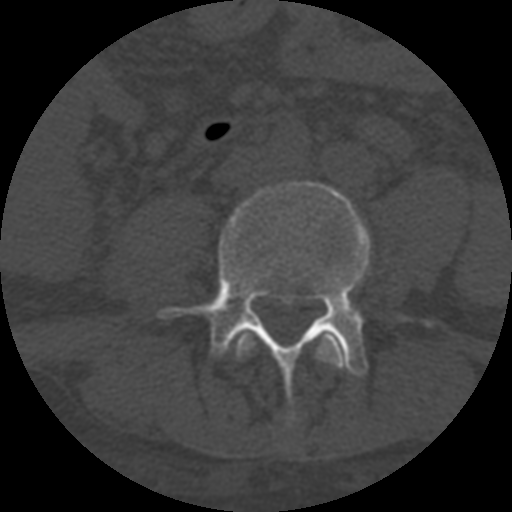
CT including the spine, one axial slice; slice 214 of 708 in the series (ordered by position); reconstruction kernel STANDARD; one of 3 acquisitions stored at this slice position; bone window (W 1800 / L 400 HU); 512 × 512 image matrix, field of view 160 × 160 mm. Patient age 55 years. Case-level facts recorded for this patient, not image findings: primary cancer: colon; vertebrae with lytic lesions (as recorded): T12, L1, L5.
Annotated regions visible in this slice (semi-automatically segmented with operator editing):
- L3 vertebra: bounding box (x1, y1, x2, y2) in pixels: (236, 332, 346, 369)
- L4 vertebra: (160, 181, 371, 397)